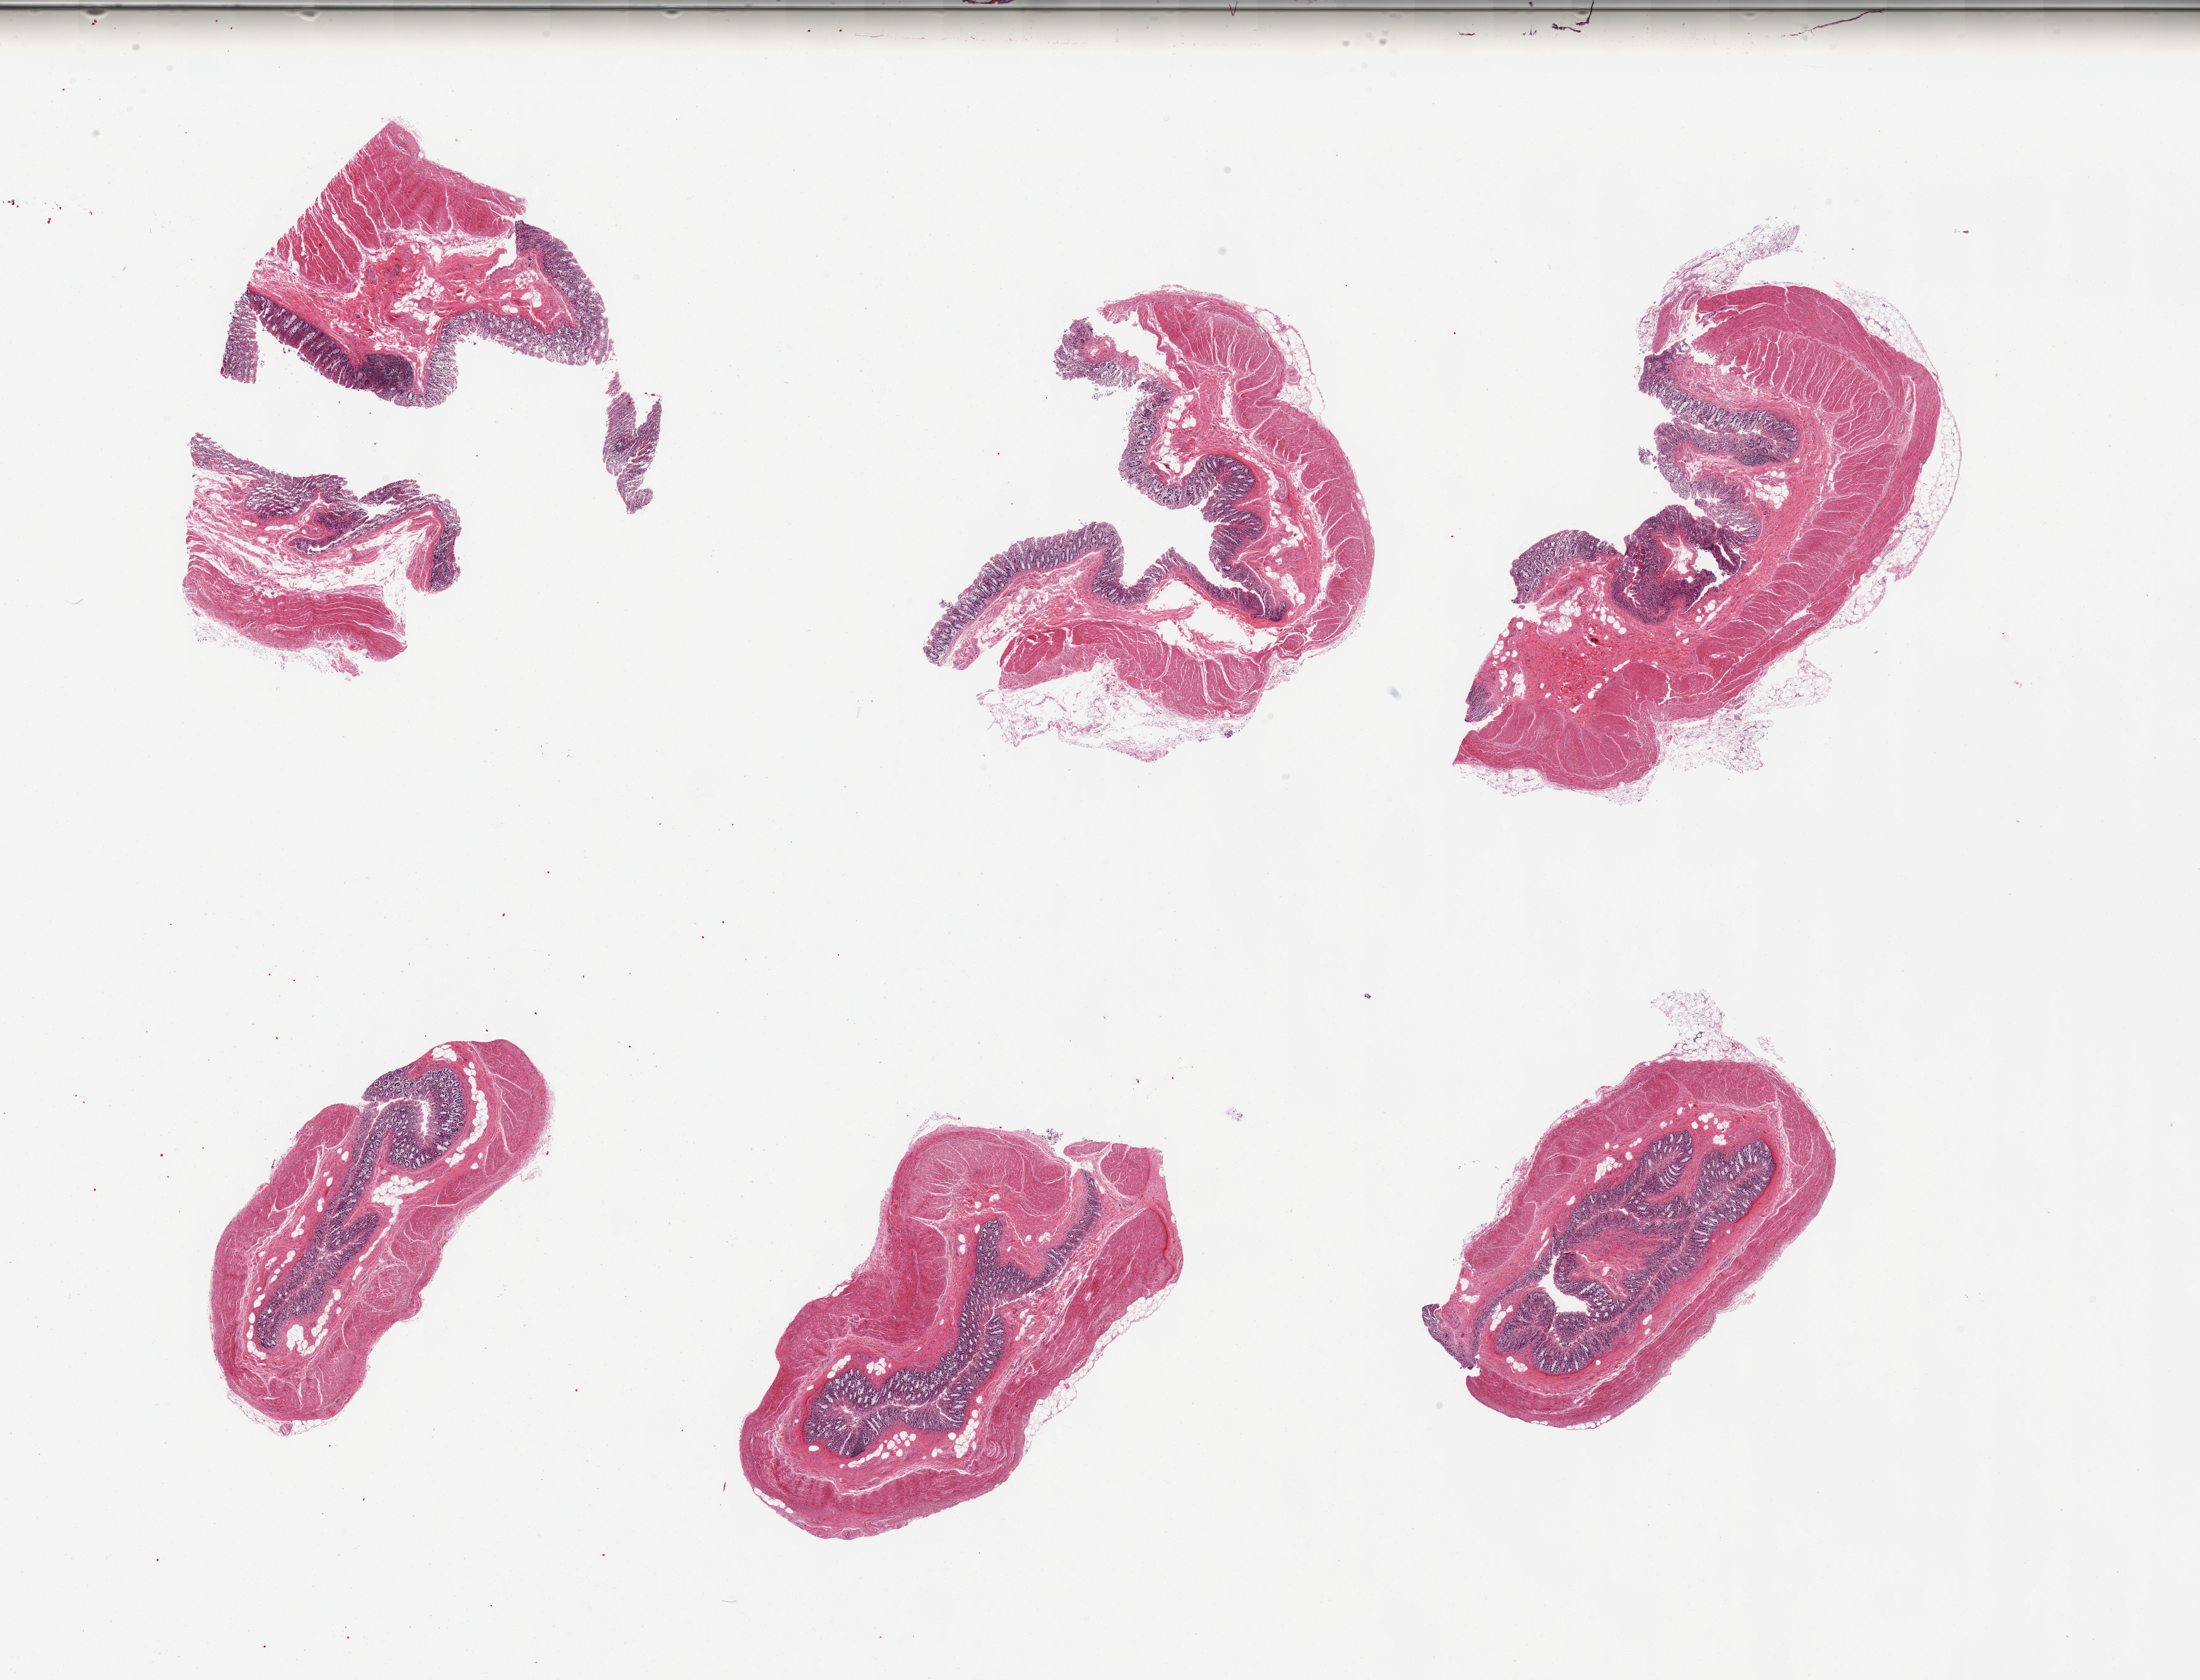
Whole-slide image, hematoxylin and eosin (H&E) stain — shown as a low-resolution overview of the whole scanned area (about 27.6 x 21.0 mm, from a 20x scan); PAXgene-fixed, paraffin-embedded tissue; section of transverse colon (target tissue); donor tissue sample. Donor sex: male.
- reviewer comment on this tissue sample: 6 pieces; mucosal autolysis varies from moderate to severe, muscularis from slight to moderate